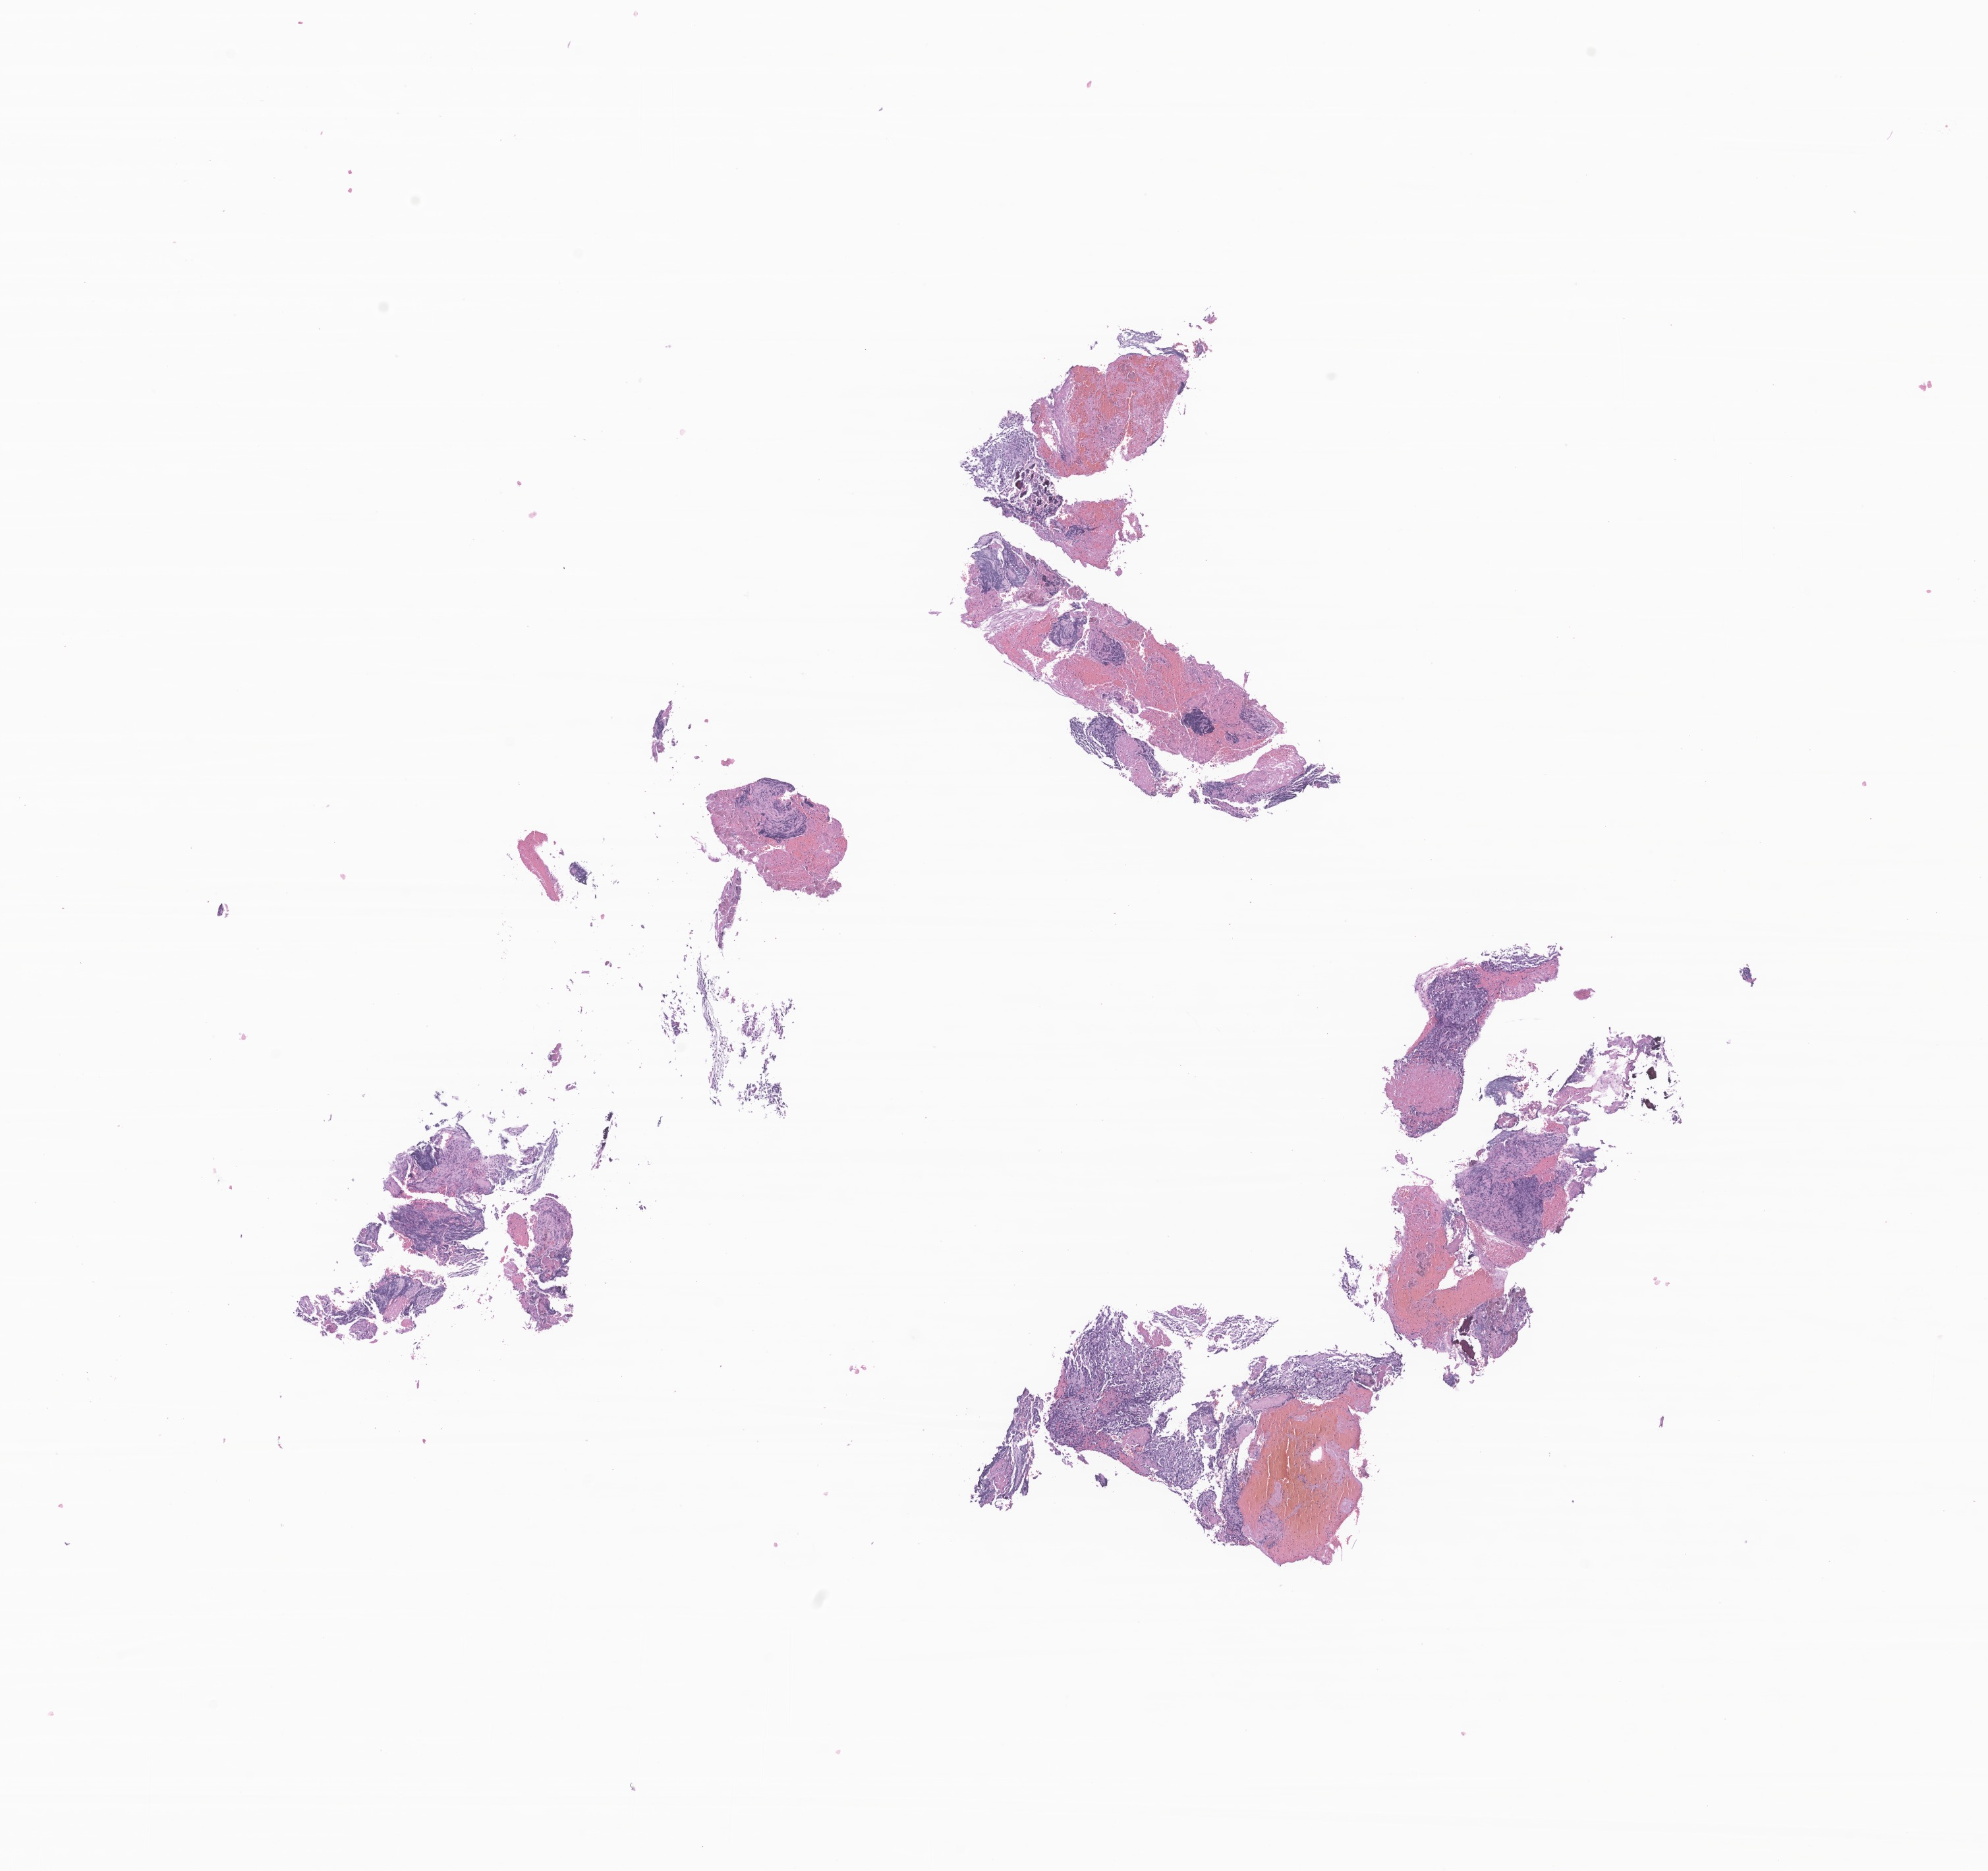
H&E whole-slide image of tumor tissue from the cerebrum, low-resolution overview of the scanned area, about 12.7 x 12.0 mm. Formalin-fixed, paraffin-embedded (FFPE) tissue. Patient female; age 585 days.
Diagnosis (ICD-O-3 morphology term): Atypical teratoid/rhabdoid tumor.